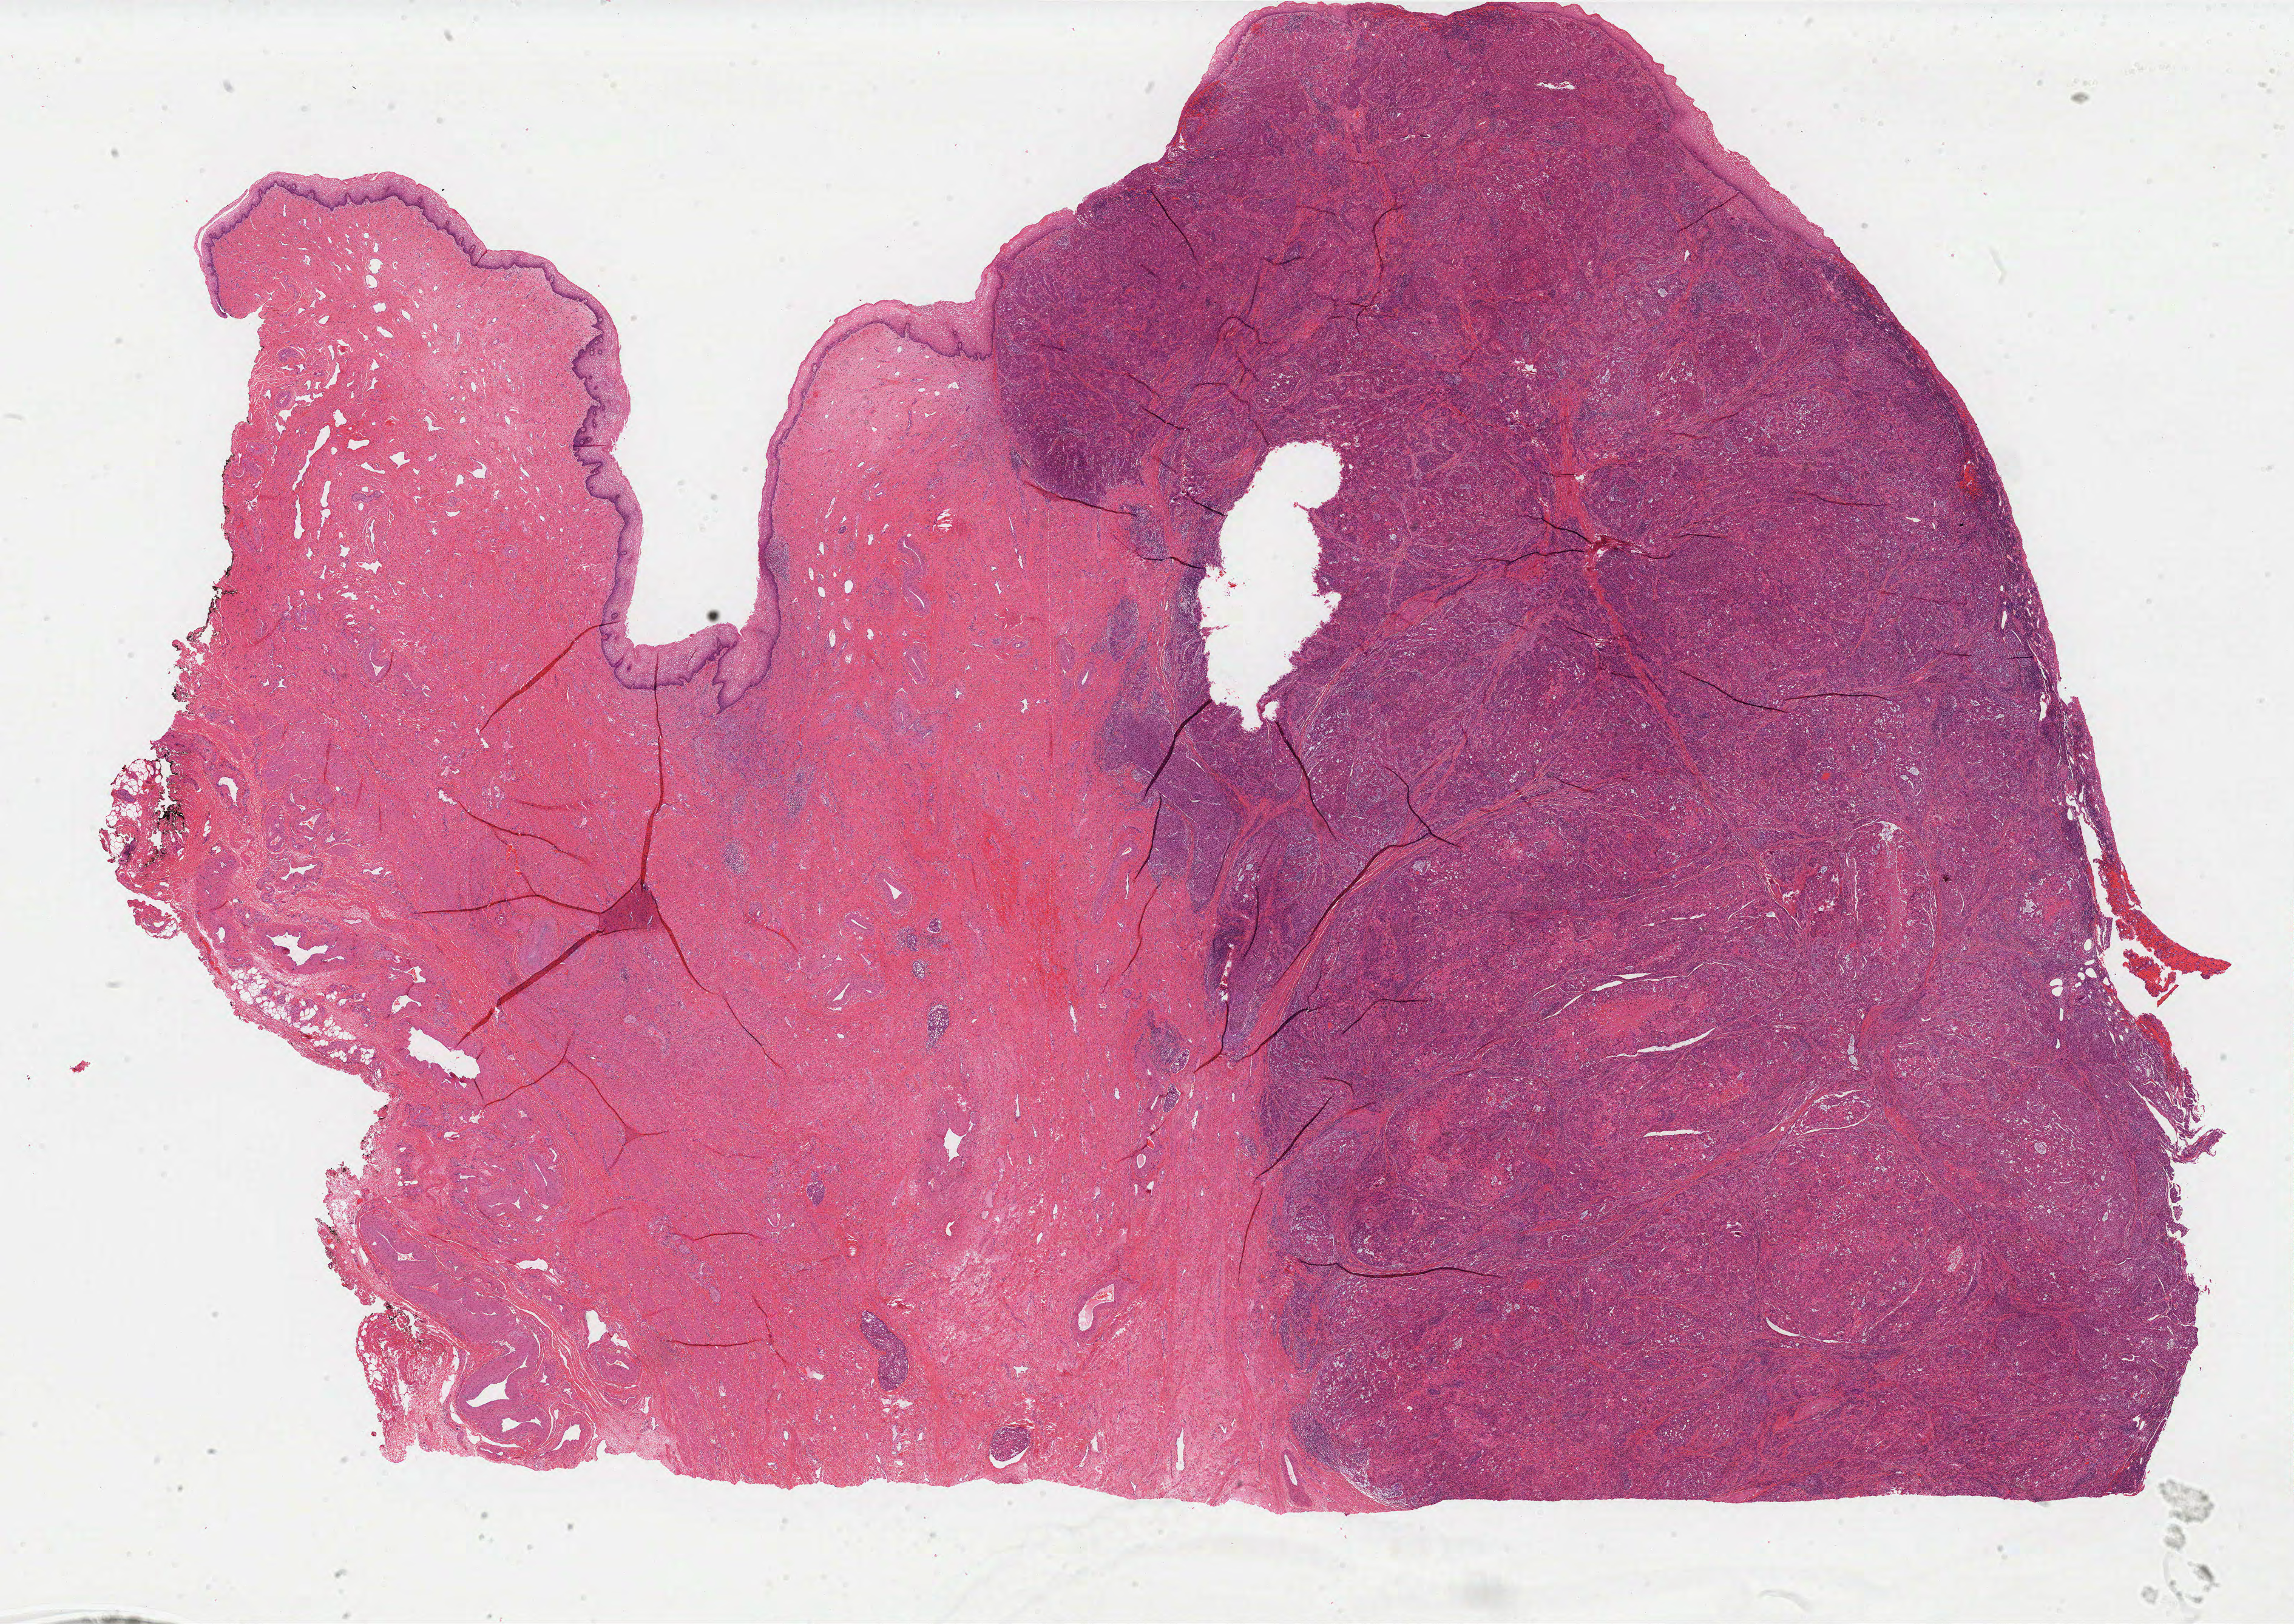
Whole-slide histology image, H&E-stained — a low-resolution overview of the entire scanned area, about 30.3 x 21.4 mm (from a 40x scan); formalin-fixed paraffin-embedded (FFPE) diagnostic section; sample: primary tumour, cervix. Patient: female, age at initial diagnosis 34 years. Histologic grade: G3 (poorly differentiated).
FIGO stage: IB2. Lymph nodes positive (case pathology): 6 of 54 examined. Pathologic diagnosis: Squamous cell carcinoma, NOS.